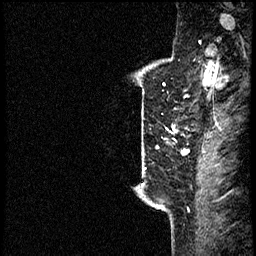
Breast MRI (dynamic contrast-enhanced), one sagittal slice. Slice 51 of 60 in the series (ordered by position). Dynamic contrast-enhanced study with each time point stored as its own series, time point 2 of 4 at this slice position (early post-contrast, ordered by acquisition time). 1.5 T. TE 4.2 ms, TR 17.6 ms. 256 × 256 image matrix, field of view 200 × 200 mm. Female patient, age 40 years. From the clinical record (not read from this slice): setting: breast cancer imaged before/during neoadjuvant chemotherapy; receptor status: HER2-positive.
Structures marked on this image (semi-automatically segmented with operator editing):
- analysis volume of interest (the breast-tissue region the enhancement analysis was run in; not a lesion): bounding box [x1, y1, x2, y2] px = [133, 56, 197, 205]
- tumour enhancement mask (voxels above the 100 % enhancement threshold inside the analysis volume of interest): [141, 118, 190, 170]